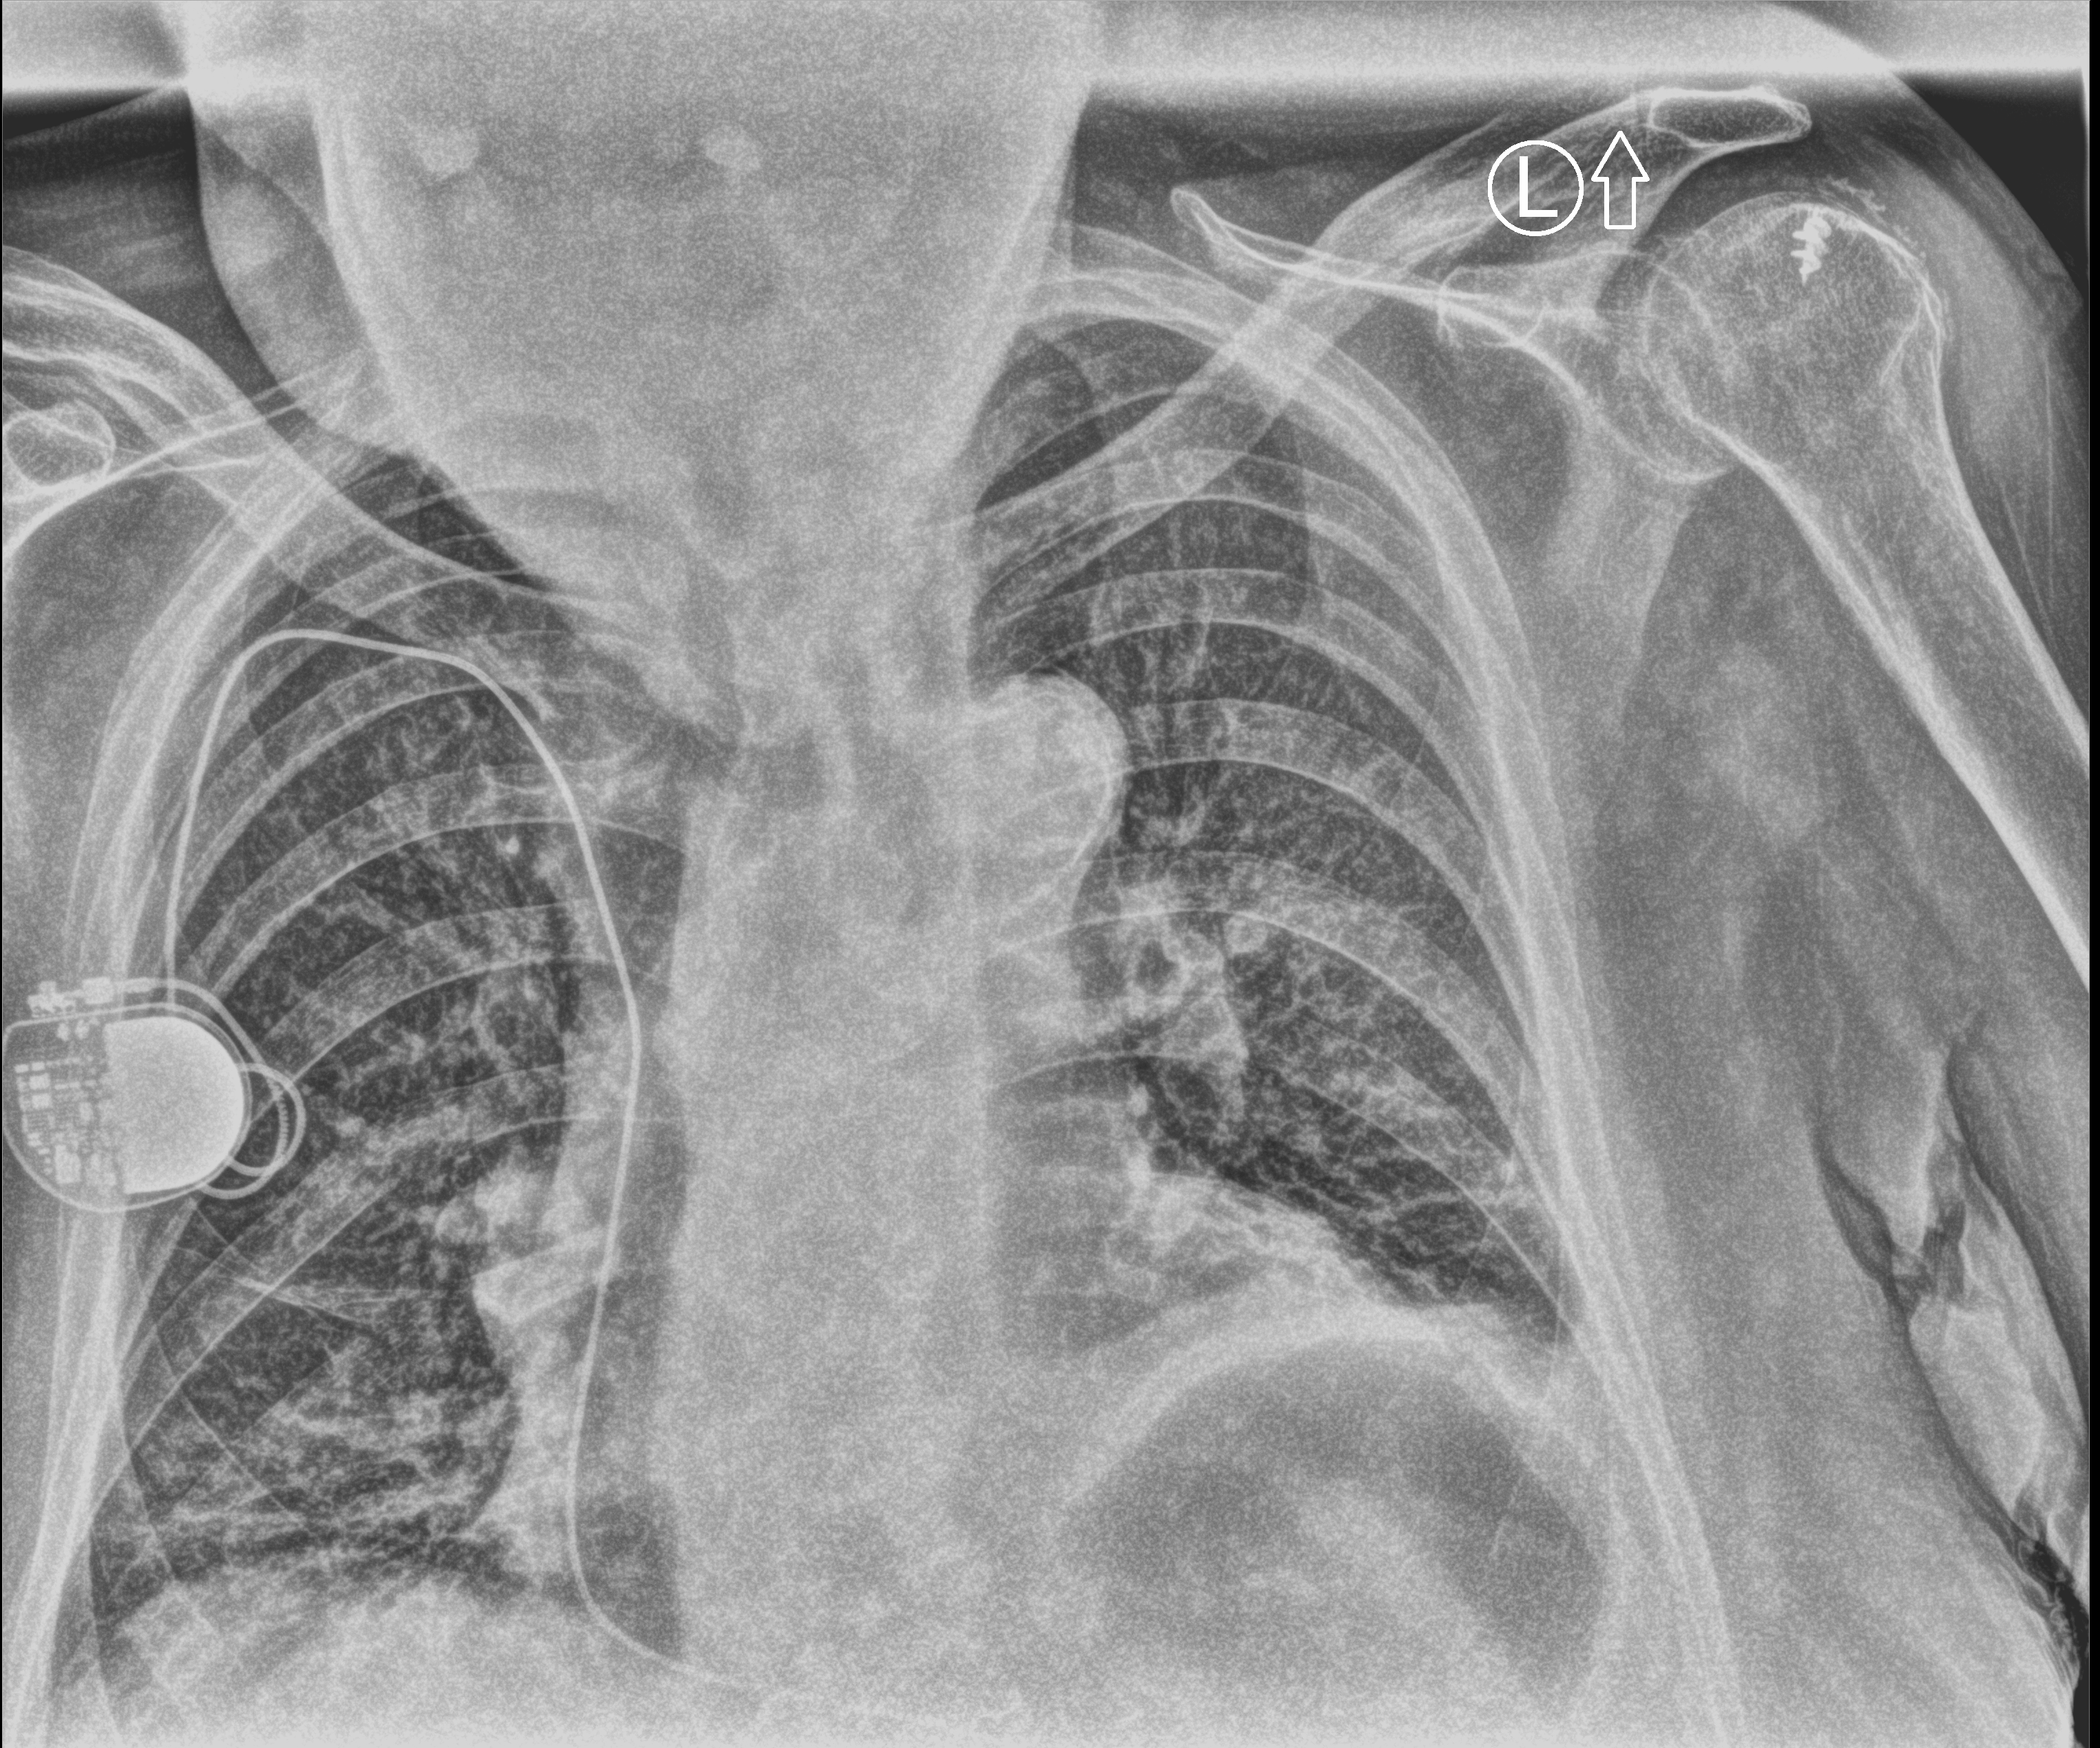
Portable chest radiograph; anteroposterior (AP) projection. Patient hospitalised with COVID-19; male, aged 75–90 years.
From the hospital-stay record, not from the radiograph (when in the stay this image was taken is not recorded): admitted to intensive care during this hospital stay: no; mechanically ventilated during this hospital stay: no.